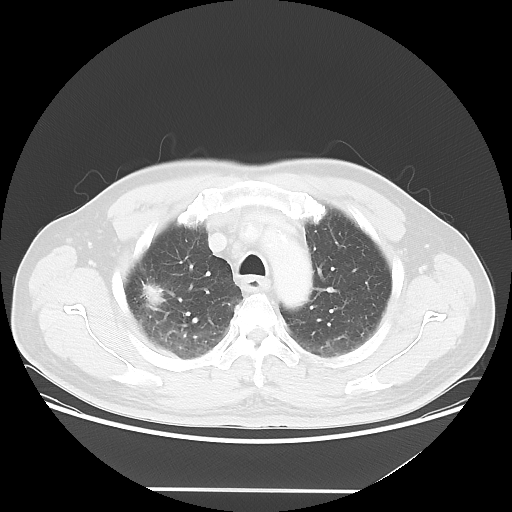
Chest CT, one axial slice; position 42 of 54 along the scan axis; 120 kVp; lung window (W 1500 / L -600 HU); 5 mm slice thickness; 512 × 512 image matrix, field of view 416 × 416 mm. Patient: male, 65 years. Case-level facts recorded for this patient, not image findings: clinical TNM (as recorded): T1c N1 M0.
Annotated regions visible in this slice (rectangle marked by the reading radiologist):
- lung tumour (recorded histology: adenocarcinoma): box from (x=142, y=276) to (x=164, y=310) px